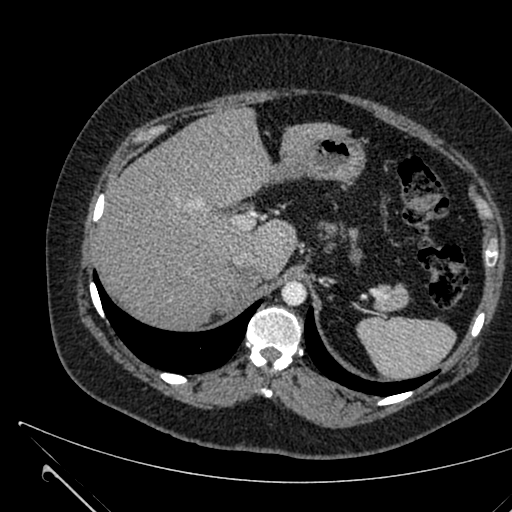
Contrast-enhanced abdominal CT, one axial slice; position 482 of 731 along the scan axis; intravenous contrast given; soft-tissue window (W 400 / L 40 HU); 1 mm slice thickness; 512 × 512 image matrix, field of view 376 × 376 mm. Female patient, age 36 years. Case-level facts recorded for this patient, not image findings: diagnosis: adrenocortical carcinoma; tumour side: right adrenal; tumour size at pathology: 10 cm; Ki-67 index: 20 %; stage (as recorded): 4.
Annotated regions visible in this slice (semi-automatically segmented with operator editing):
- mass: box from (x=220, y=274) to (x=256, y=312) px